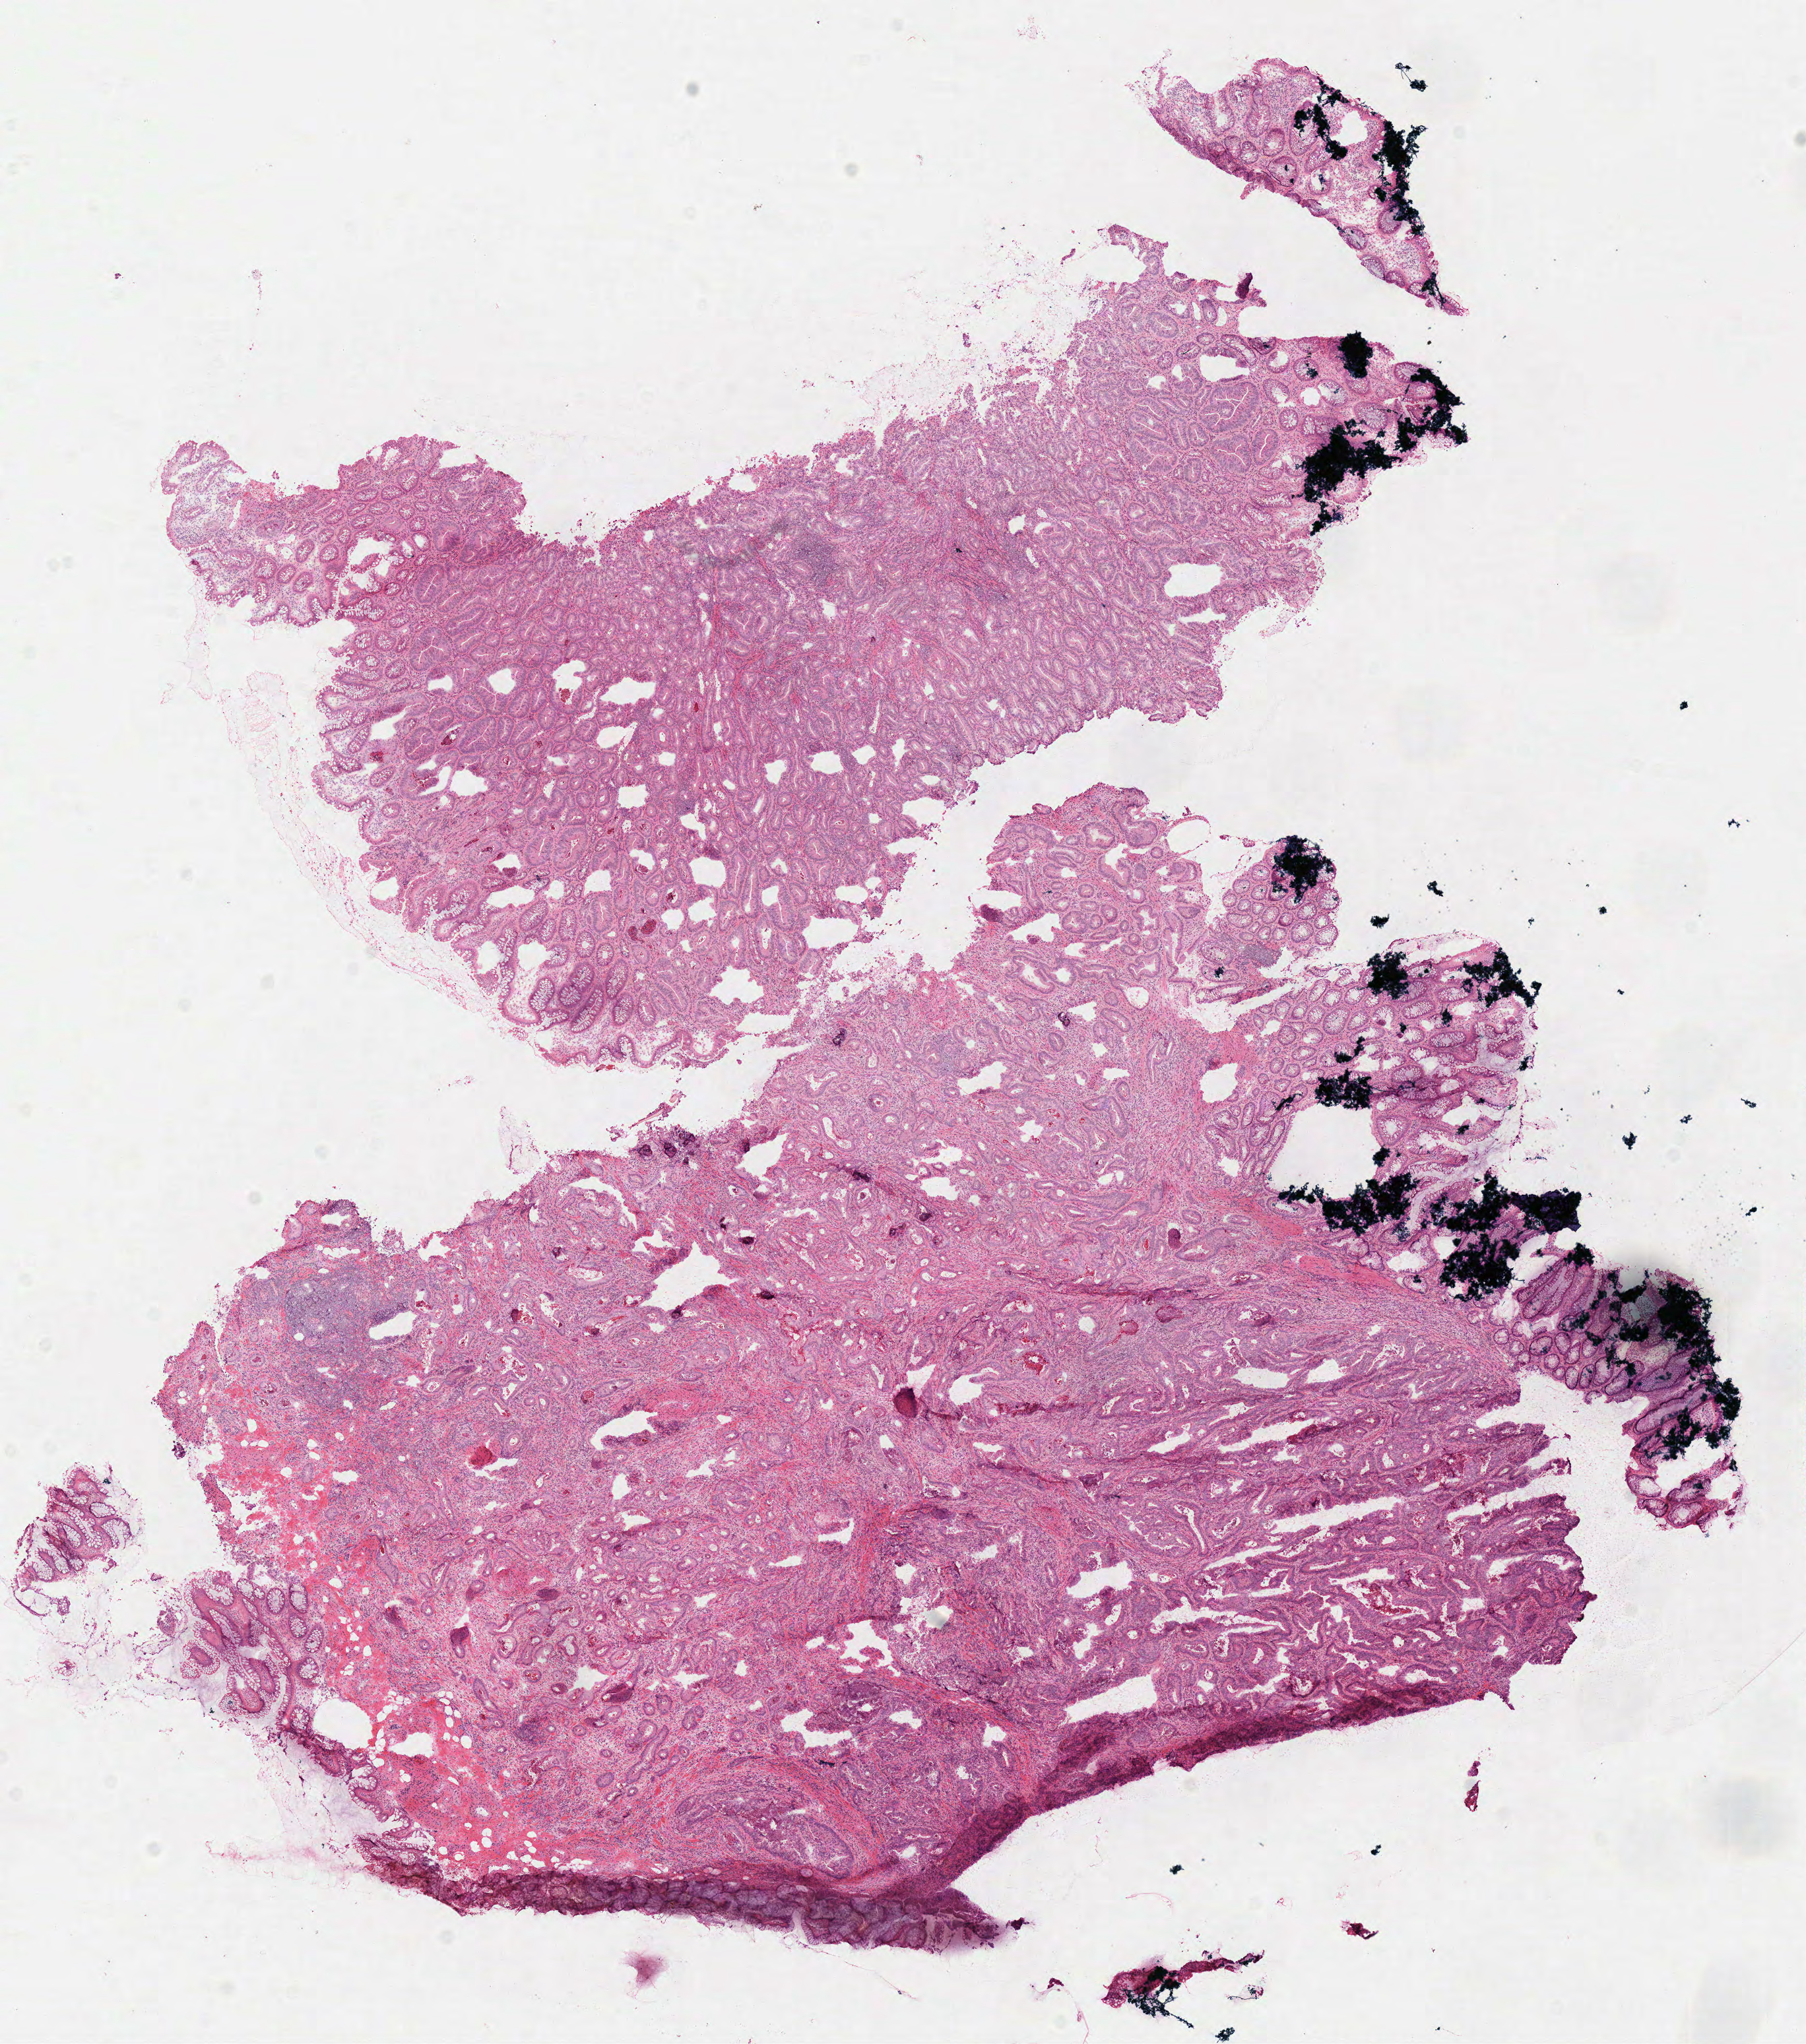
Whole-slide histology image, H&E-stained — whole scanned area (about 10.8 x 12.2 mm) shown as a low-resolution overview; frozen section; sample: primary tumour, colon. Patient: male, age at initial diagnosis 74 years. Pathologist review of this section (percent, as recorded): tumour cells 70%, tumour nuclei 70%, normal cells 10%, stromal cells 15%, necrosis 5%.
• lymph nodes positive (case pathology): 0 of 23 examined
• histologic diagnosis: Adenocarcinoma, NOS (sigmoid colon)
• AJCC pathologic stage: I